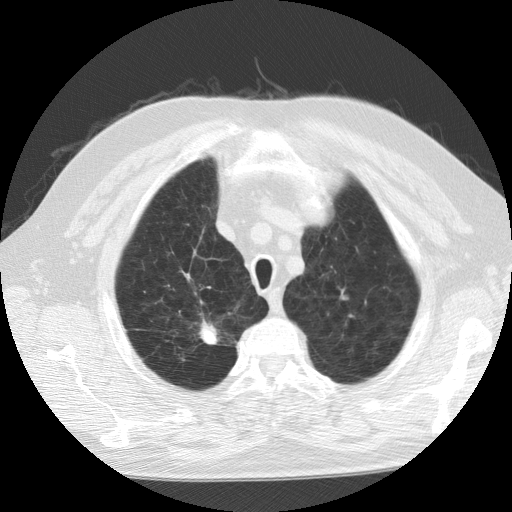
Axial slice from a low-dose chest CT screening exam. Second screening round (one year after baseline). Lung window (W 1500 / L -600 HU). 2.5 mm slice thickness. Standard (soft-tissue) reconstruction kernel (STANDARD). Male, age 64 years at enrolment. Current smoker at enrolment.
Expert-annotated lung lesion, box from (x=184, y=316) to (x=234, y=358) px. The screening reader recorded 2 non-calcified nodules or masses ≥4 mm on this exam (left upper lobe, right lower lobe); which of them this box marks is not recorded. Participant outcome: lung cancer diagnosed 233 days after this screen — squamous cell carcinoma, NOS, left upper lobe, moderately differentiated (G2), stage IA (AJCC 6th edition), 10 mm at pathology.